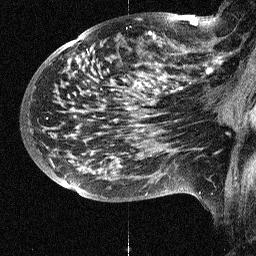
Breast MRI (dynamic contrast-enhanced), one sagittal slice. Position 39 of 64 along the scan axis. Dynamic contrast-enhanced study with each time point stored as its own series, time point 2 of 3 at this slice position (early post-contrast, ordered by acquisition time). 1.5 T. TE 4.5 ms, TR 11 ms. 2.5 mm slice thickness. 256 × 256 image matrix, field of view 200 × 200 mm. Patient: female, 38 years. From the clinical record (not read from this slice): setting: breast cancer imaged before/during neoadjuvant chemotherapy; receptor status: HR-positive, HER2-negative.
Structures marked on this image (semi-automatic segmentation, software-assisted and operator-edited):
- analysis volume of interest (the breast-tissue region the enhancement analysis was run in; not a lesion): bounding box [x1, y1, x2, y2] px = [88, 18, 252, 126]
- tumour enhancement mask (voxels above the 90 % enhancement threshold inside the analysis volume of interest): [149, 21, 222, 74]